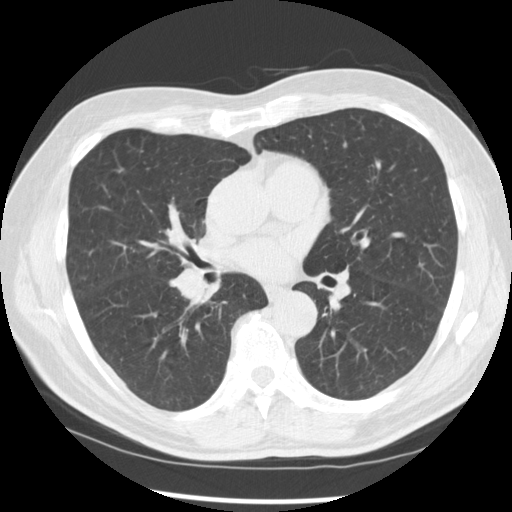
Low-dose screening chest CT, one axial slice. Slice 146 of 277 in the series (ordered by position). Lung window (W 1500 / L -600 HU). 2.5 mm slice thickness. 512 × 512 image matrix, field of view 365 × 365 mm.
Structures marked on this image (manually delineated by an expert):
- lesion 1 (tumor, middle lobe of right lung): bounding box (x1, y1, x2, y2) in pixels: (173, 267, 208, 303)